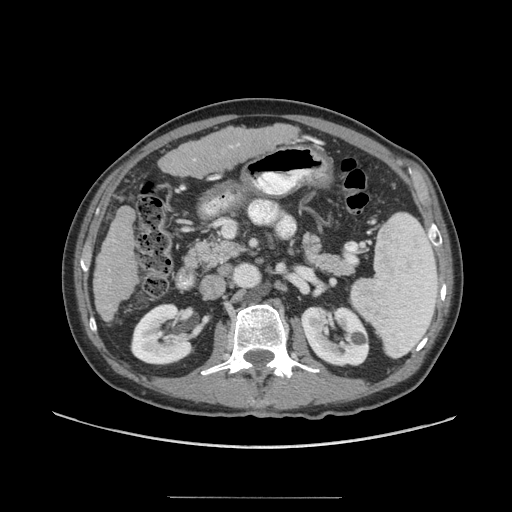
Contrast-enhanced abdominal CT (liver protocol), one axial slice; position 20 of 71 along the scan axis; soft-tissue window (W 400 / L 40 HU); 512 × 512 image matrix, field of view 400 × 400 mm. From the clinical record (not read from this slice): diagnosis: hepatocellular carcinoma (patient treated with transarterial chemoembolisation; whether this scan precedes or follows treatment is not stated here); TNM stage (as recorded): Stage-I; Child-Pugh class: A; tumour differentiation: well differentiated; tumour nodularity: uninodular.
Structures marked on this image (semi-automatically segmented with operator editing):
- liver parenchyma outside the tumour (the mass and vessels are separate outlines, so this box may not span the whole liver): bounding box [x1, y1, x2, y2] px = [92, 124, 298, 322]
- liver vessels: [237, 144, 239, 146]